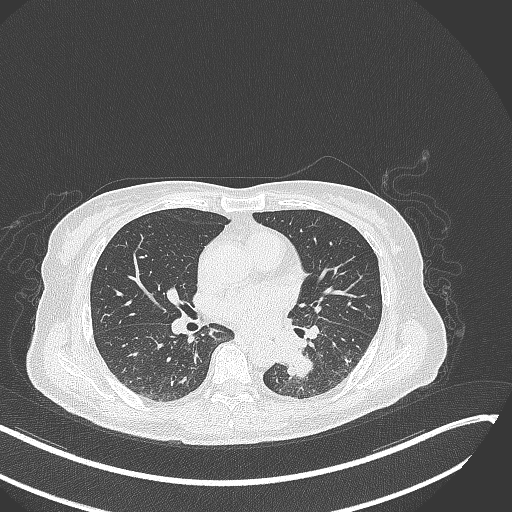
Chest CT, one axial slice. Slice 133 of 342 in the series (ordered by position). Reconstruction kernel B70f. 120 kVp. Lung window (W 1500 / L -600 HU). 1 mm slice thickness. 512 × 512 image matrix, field of view 400 × 400 mm. Patient: female, 64 years. Case-level facts recorded for this patient, not image findings: clinical TNM (as recorded): T3 N1 M1.
Annotated regions visible in this slice (bounding box drawn by a radiologist):
- lung tumour (recorded histology: small cell carcinoma): bounding box (x1, y1, x2, y2) in pixels: (263, 322, 320, 383)